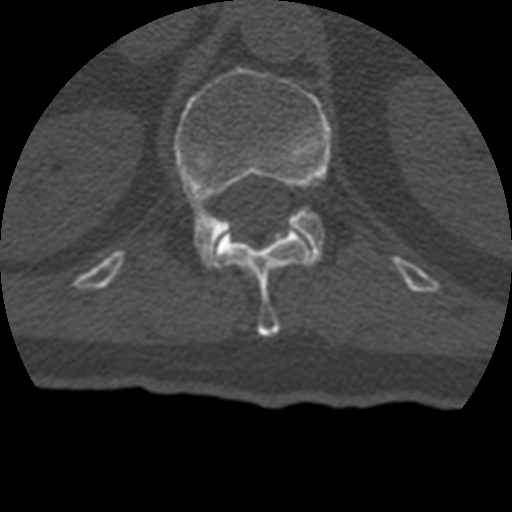
CT including the spine, one axial slice; 120 kVp; bone window (W 1800 / L 400 HU); 1.25 mm slice thickness; 512 × 512 image matrix, field of view 160 × 160 mm. Patient age 69 years. Case-level facts recorded for this patient, not image findings: primary cancer: prostate.
Annotated regions visible in this slice (semi-automatic segmentation, software-assisted and operator-edited):
- L1 vertebra: bounding box (x1, y1, x2, y2) in pixels: (174, 67, 332, 269)
- T12 vertebra: (214, 224, 314, 337)